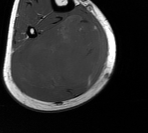
MRI of an extremity soft-tissue mass, one axial slice. Position 65 of 76 along the scan axis. MR volume resampled by the dataset authors to the PET/CT grid (not the native acquisition matrix). 3.27 mm slice thickness. 148 × 133 image matrix, field of view 145 × 130 mm. Male patient. Case-level facts recorded for this patient, not image findings: histological type: liposarcoma - round cell; grade: high; site of the primary tumour: right calf.
Structures marked on this image (expert contour drawn on MRI and transferred to this co-registered scan by the dataset authors):
- gross tumour volume (mass): bounding box [x1, y1, x2, y2] px = [15, 19, 103, 91]